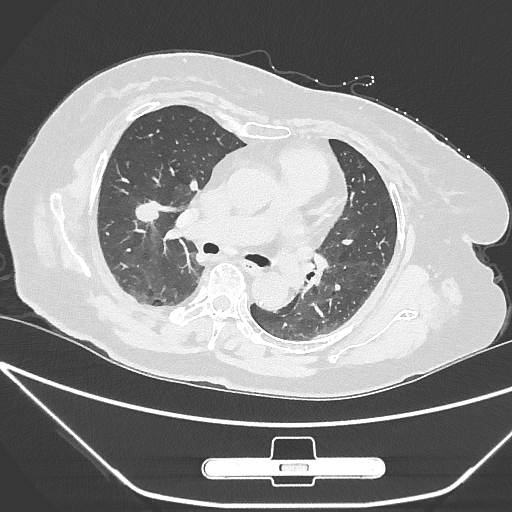
Chest CT, one axial slice; position 158 of 245 along the scan axis; 120 kVp; lung window (W 1500 / L -600 HU); 1 mm slice thickness; 512 × 512 image matrix. Patient: female, 65 years. From the clinical record (not read from this slice): clinical TNM (as recorded): T1c N0 M0; histopathological grade: G3.
Structures marked on this image (bounding box drawn by a radiologist):
- lung tumour (recorded histology: adenocarcinoma): bounding box <137,197,164,224> (left, top, right, bottom; pixels)